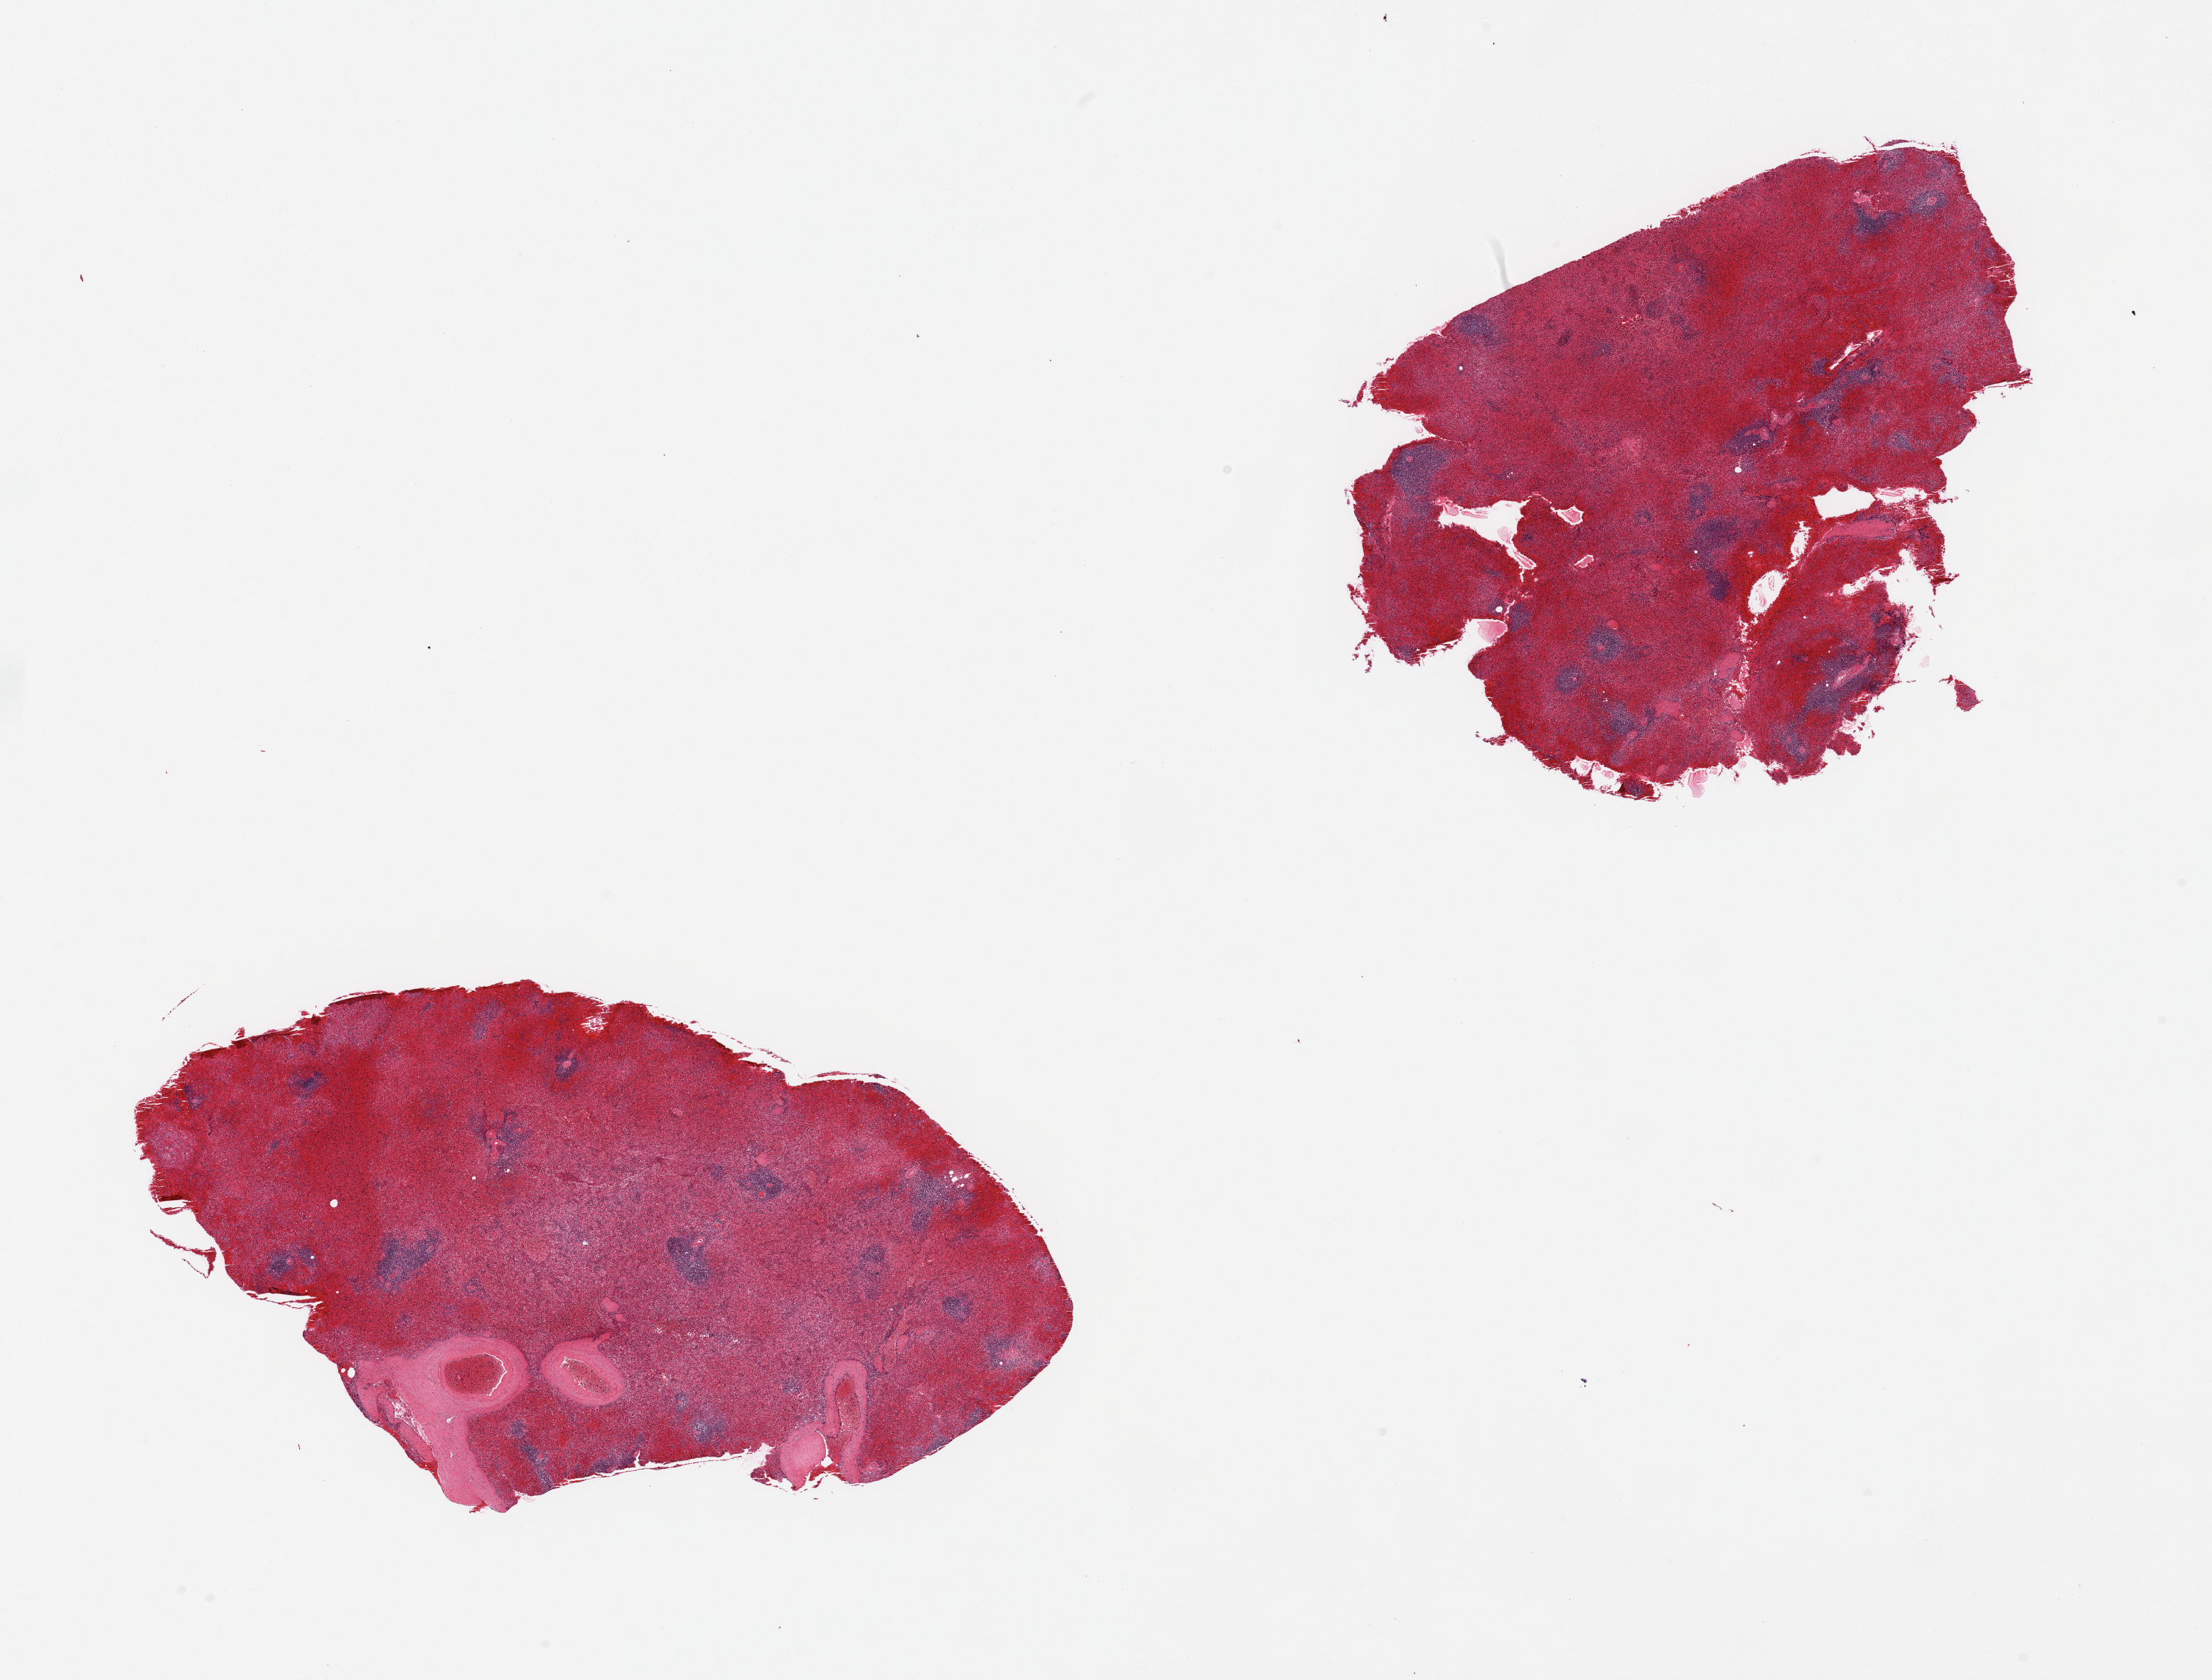
Haematoxylin and eosin whole-slide image — low-resolution overview of the scanned area, about 24.6 x 18.7 mm (slide scanned at 20x), PAXgene-fixed paraffin-embedded (PFPE) section, target tissue: spleen, tissue donor sample. Donor: female.
Review note (as recorded): 2 pieces, marked congestion.